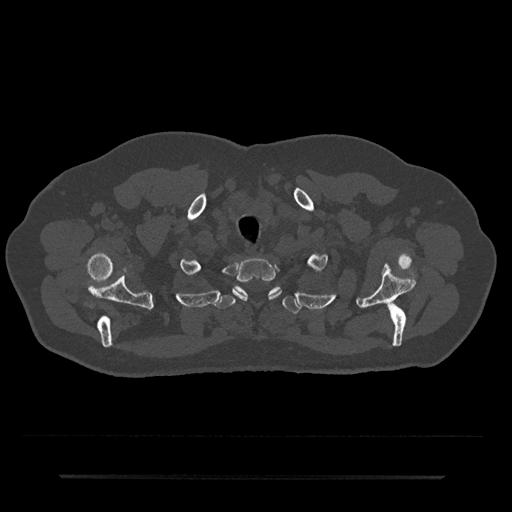
CT including the spine, one axial slice; slice 626 of 797 in the series (ordered by position); bone window (W 1800 / L 400 HU); 0.5 mm slice thickness; 512 × 512 image matrix, field of view 437 × 437 mm. Male patient, age 69 years. From the clinical record (not read from this slice): primary cancer: prostate.
Structures marked on this image (semi-automatic segmentation, software-assisted and operator-edited):
- T1 vertebra: bounding box (x1, y1, x2, y2) in pixels: (233, 258, 281, 300)
- T2 vertebra: (216, 286, 301, 314)